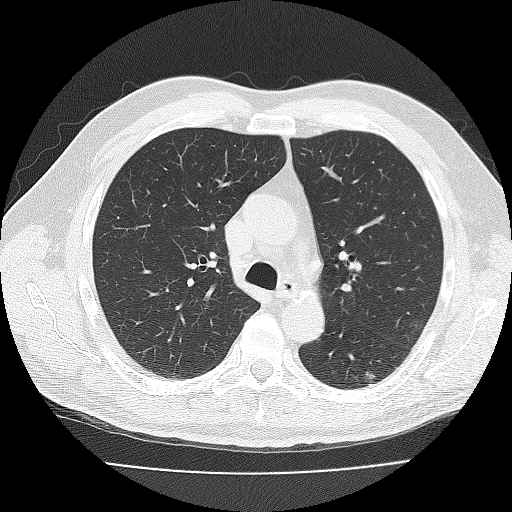
Axial slice from a low-dose chest CT screening exam; second annual screen; lung window (W 1500 / L -600 HU); 3 mm slice thickness; slice 32 of 96 in the series. Male participant, aged 65 years at enrolment. Former smoker at enrolment.
- Lesion marked by an expert reader, bounding box <350,357,391,392> (left, top, right, bottom; pixels).
- Reader record for this screening exam (exam-level; its link to the box is not recorded): non-calcified nodule or mass ≥4 mm, left lower lobe, 11 × 10 mm, smooth margins, soft tissue attenuation, pre-existing on the prior screen: yes; interval growth: yes.
- Official screen result: positive, other.
- Later outcome: lung cancer diagnosed 8 days after this screen — adenocarcinoma, NOS, left lower lobe, well differentiated (G1), stage IB (AJCC 6th edition), 10 mm at pathology.